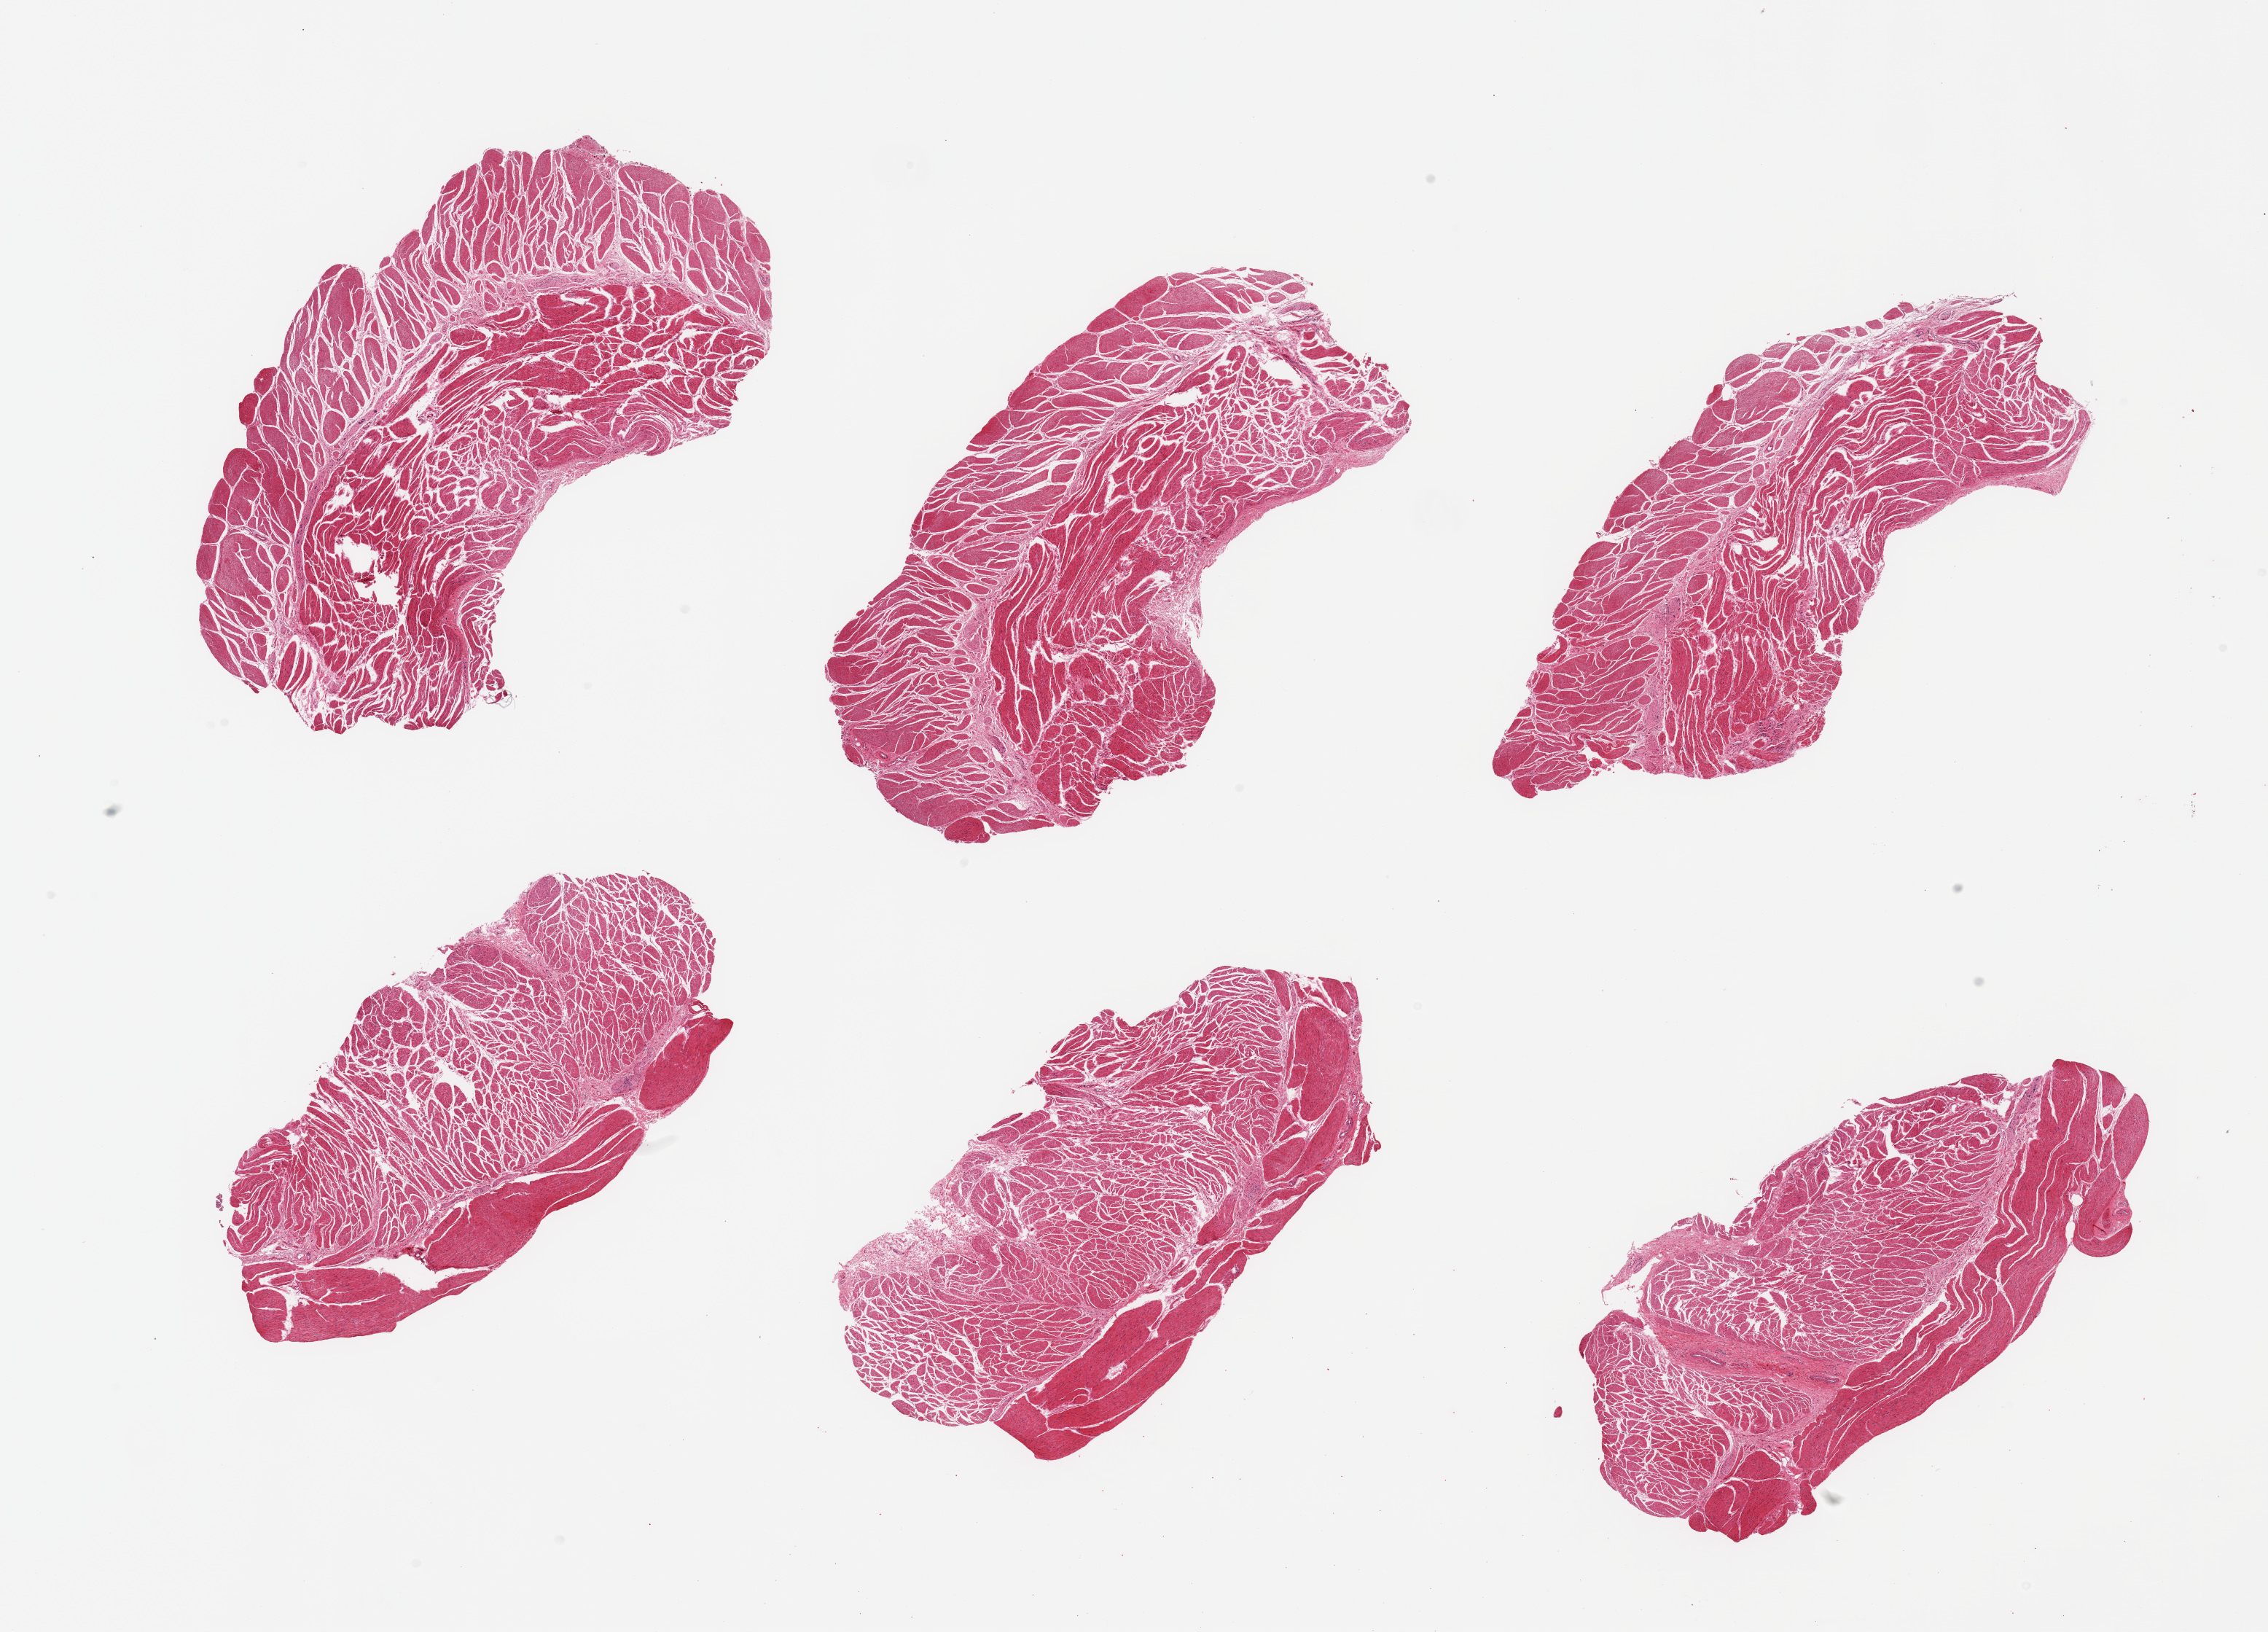
Digitized haematoxylin and eosin-stained section, brightfield, low-resolution overview of the scanned area, about 24.6 x 17.7 mm (from a 20x scan). PAXgene-fixed, paraffin-embedded tissue. Target tissue: gastroesophageal junction. Donor tissue sample. Donor sex: male.
Reviewer comment on this tissue sample: 6 pieces; well trimmed target muscularis.